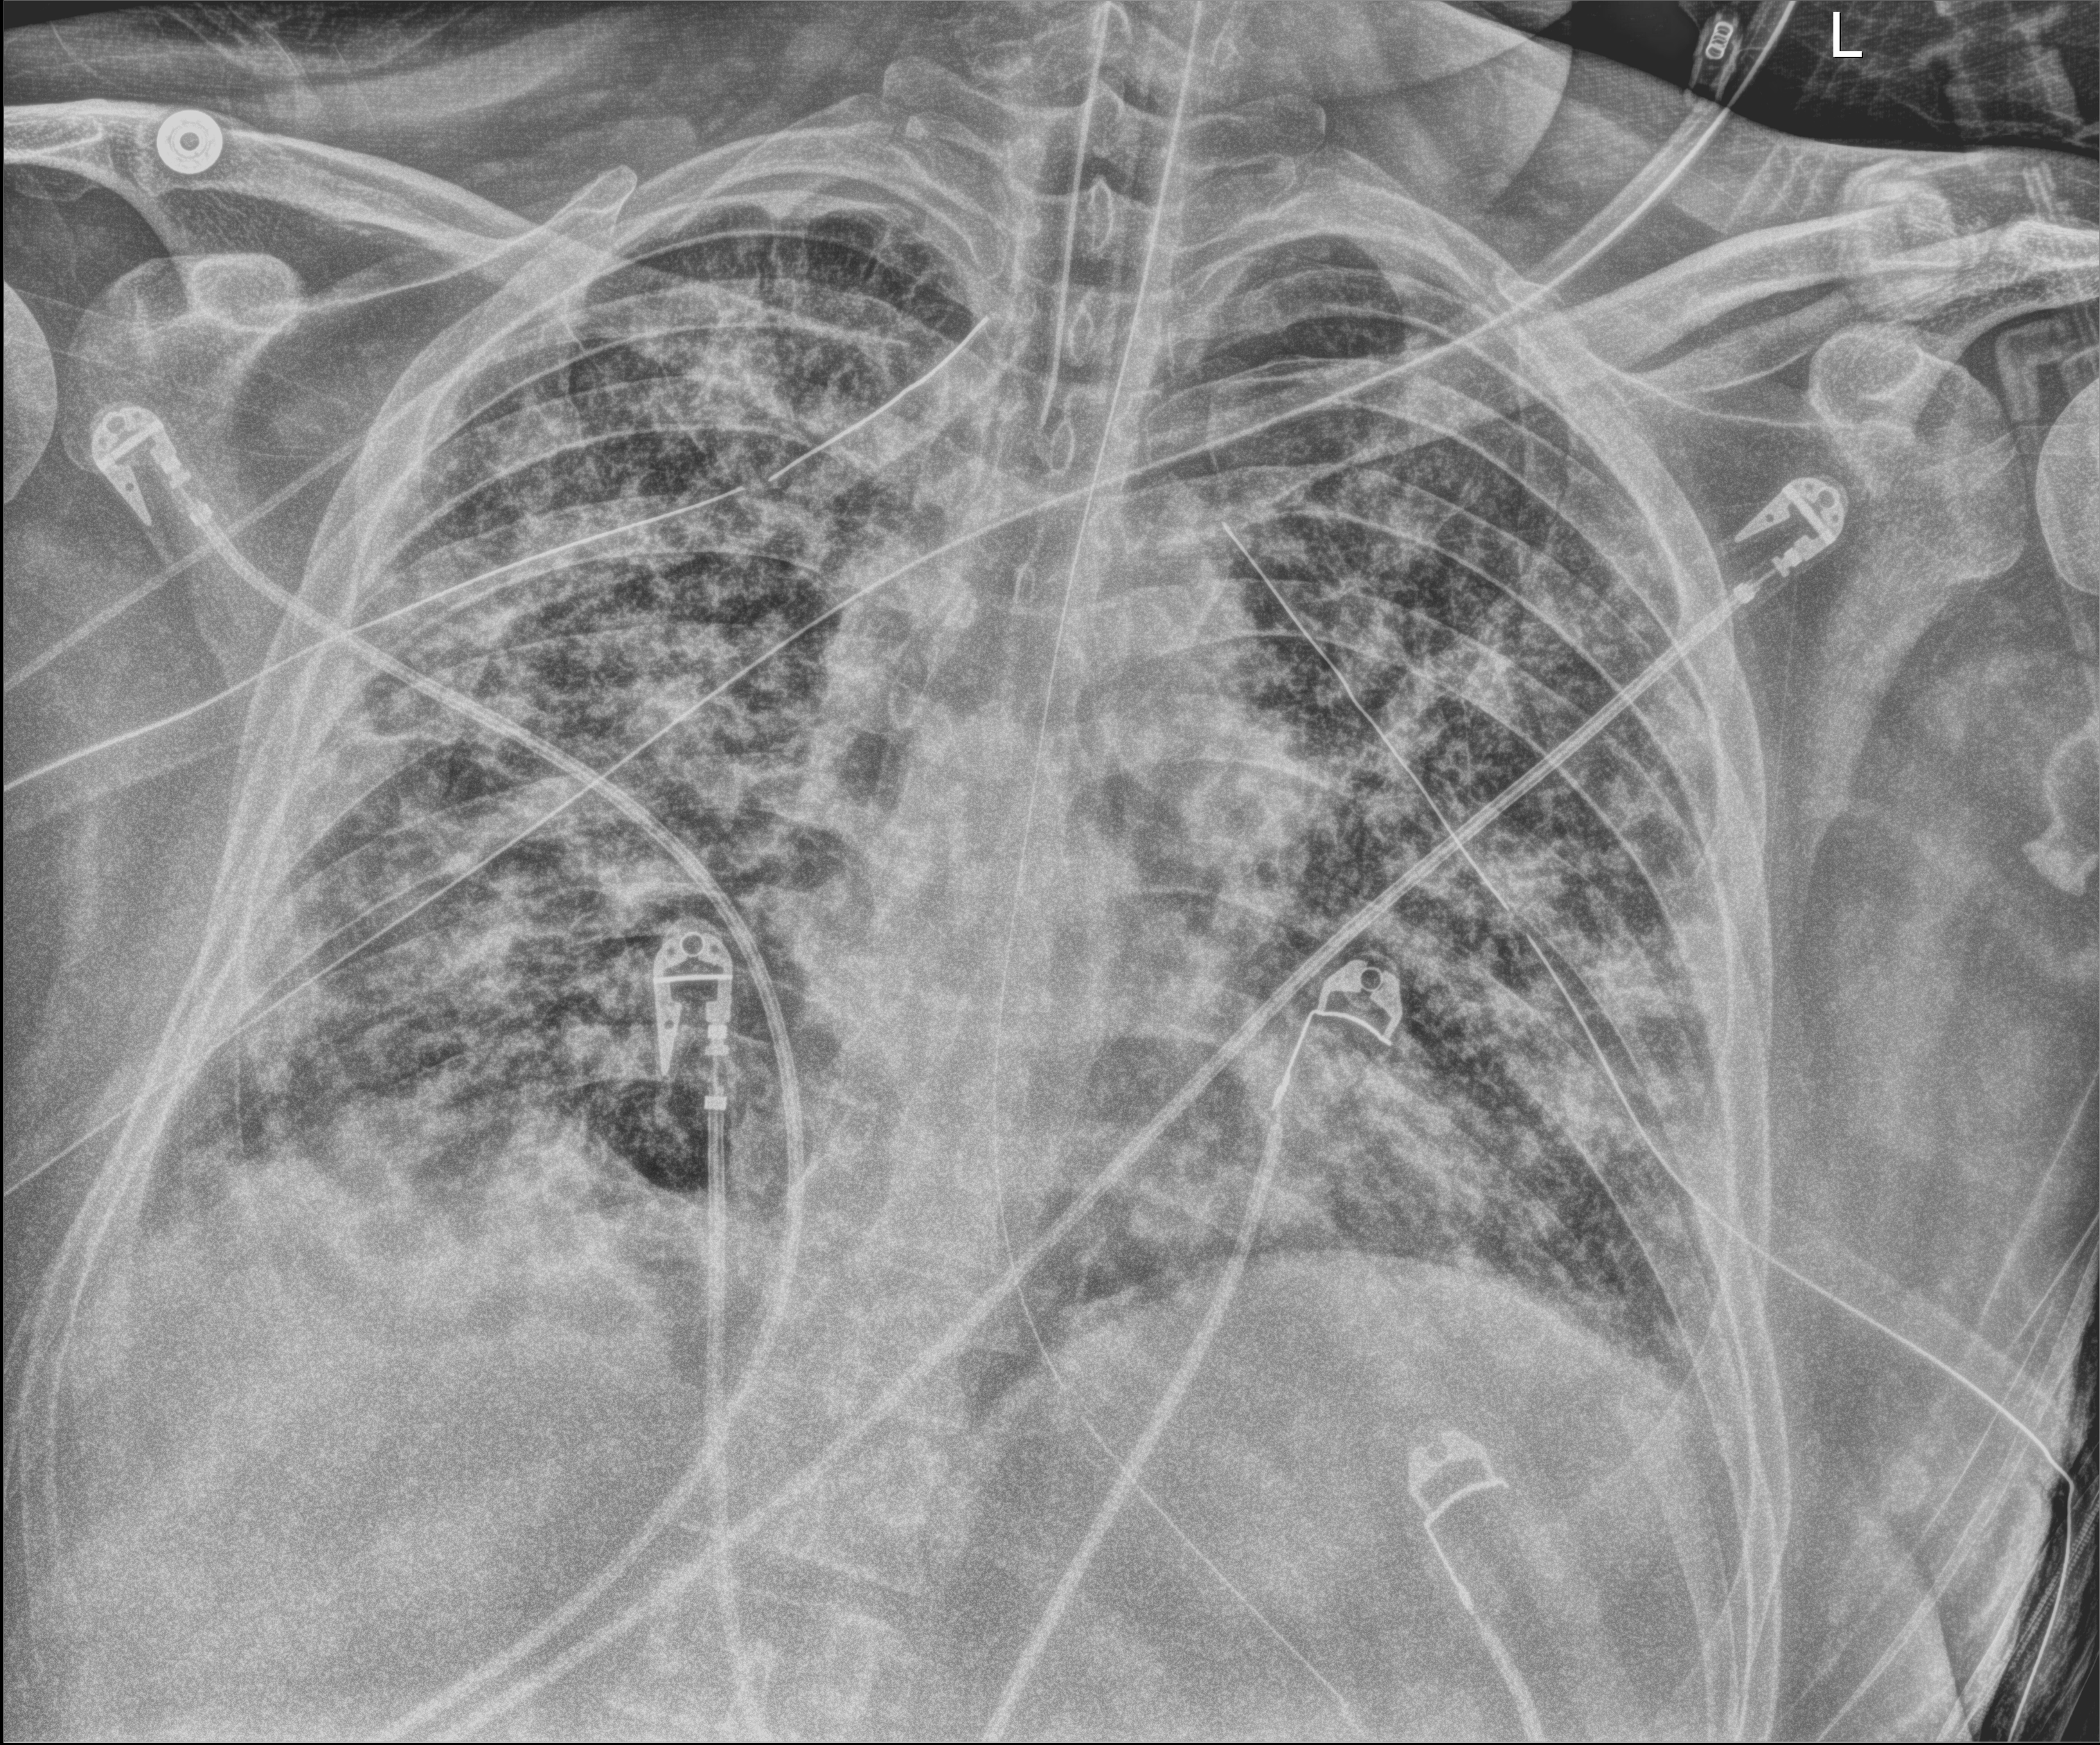
Bedside chest radiograph (digital radiography); anteroposterior (AP) projection. Male patient hospitalised with COVID-19, age 18–59 years.
From the hospital-stay record, not from the radiograph (when in the stay this image was taken is not recorded): mechanically ventilated during this hospital stay: yes.